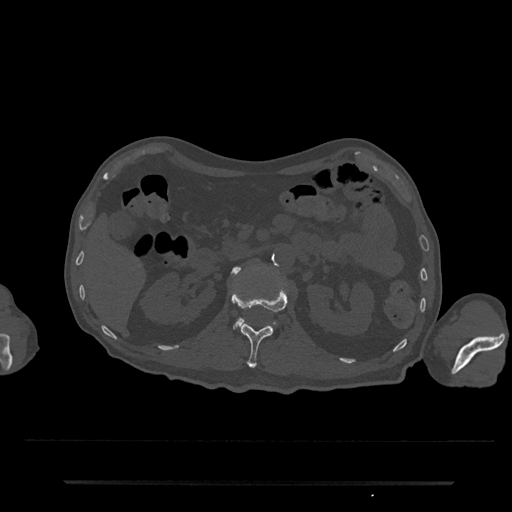
CT including the spine, one axial slice; 120 kVp; bone window (W 1800 / L 400 HU); 0.5 mm slice thickness; 512 × 512 image matrix, field of view 427 × 427 mm. Patient: male, 74 years. From the clinical record (not read from this slice): primary cancer: prostate.
Annotated regions visible in this slice (semi-automatically segmented with operator editing):
- L1 vertebra: bounding box (x1, y1, x2, y2) in pixels: (231, 284, 288, 368)
- L2 vertebra: (234, 267, 244, 327)